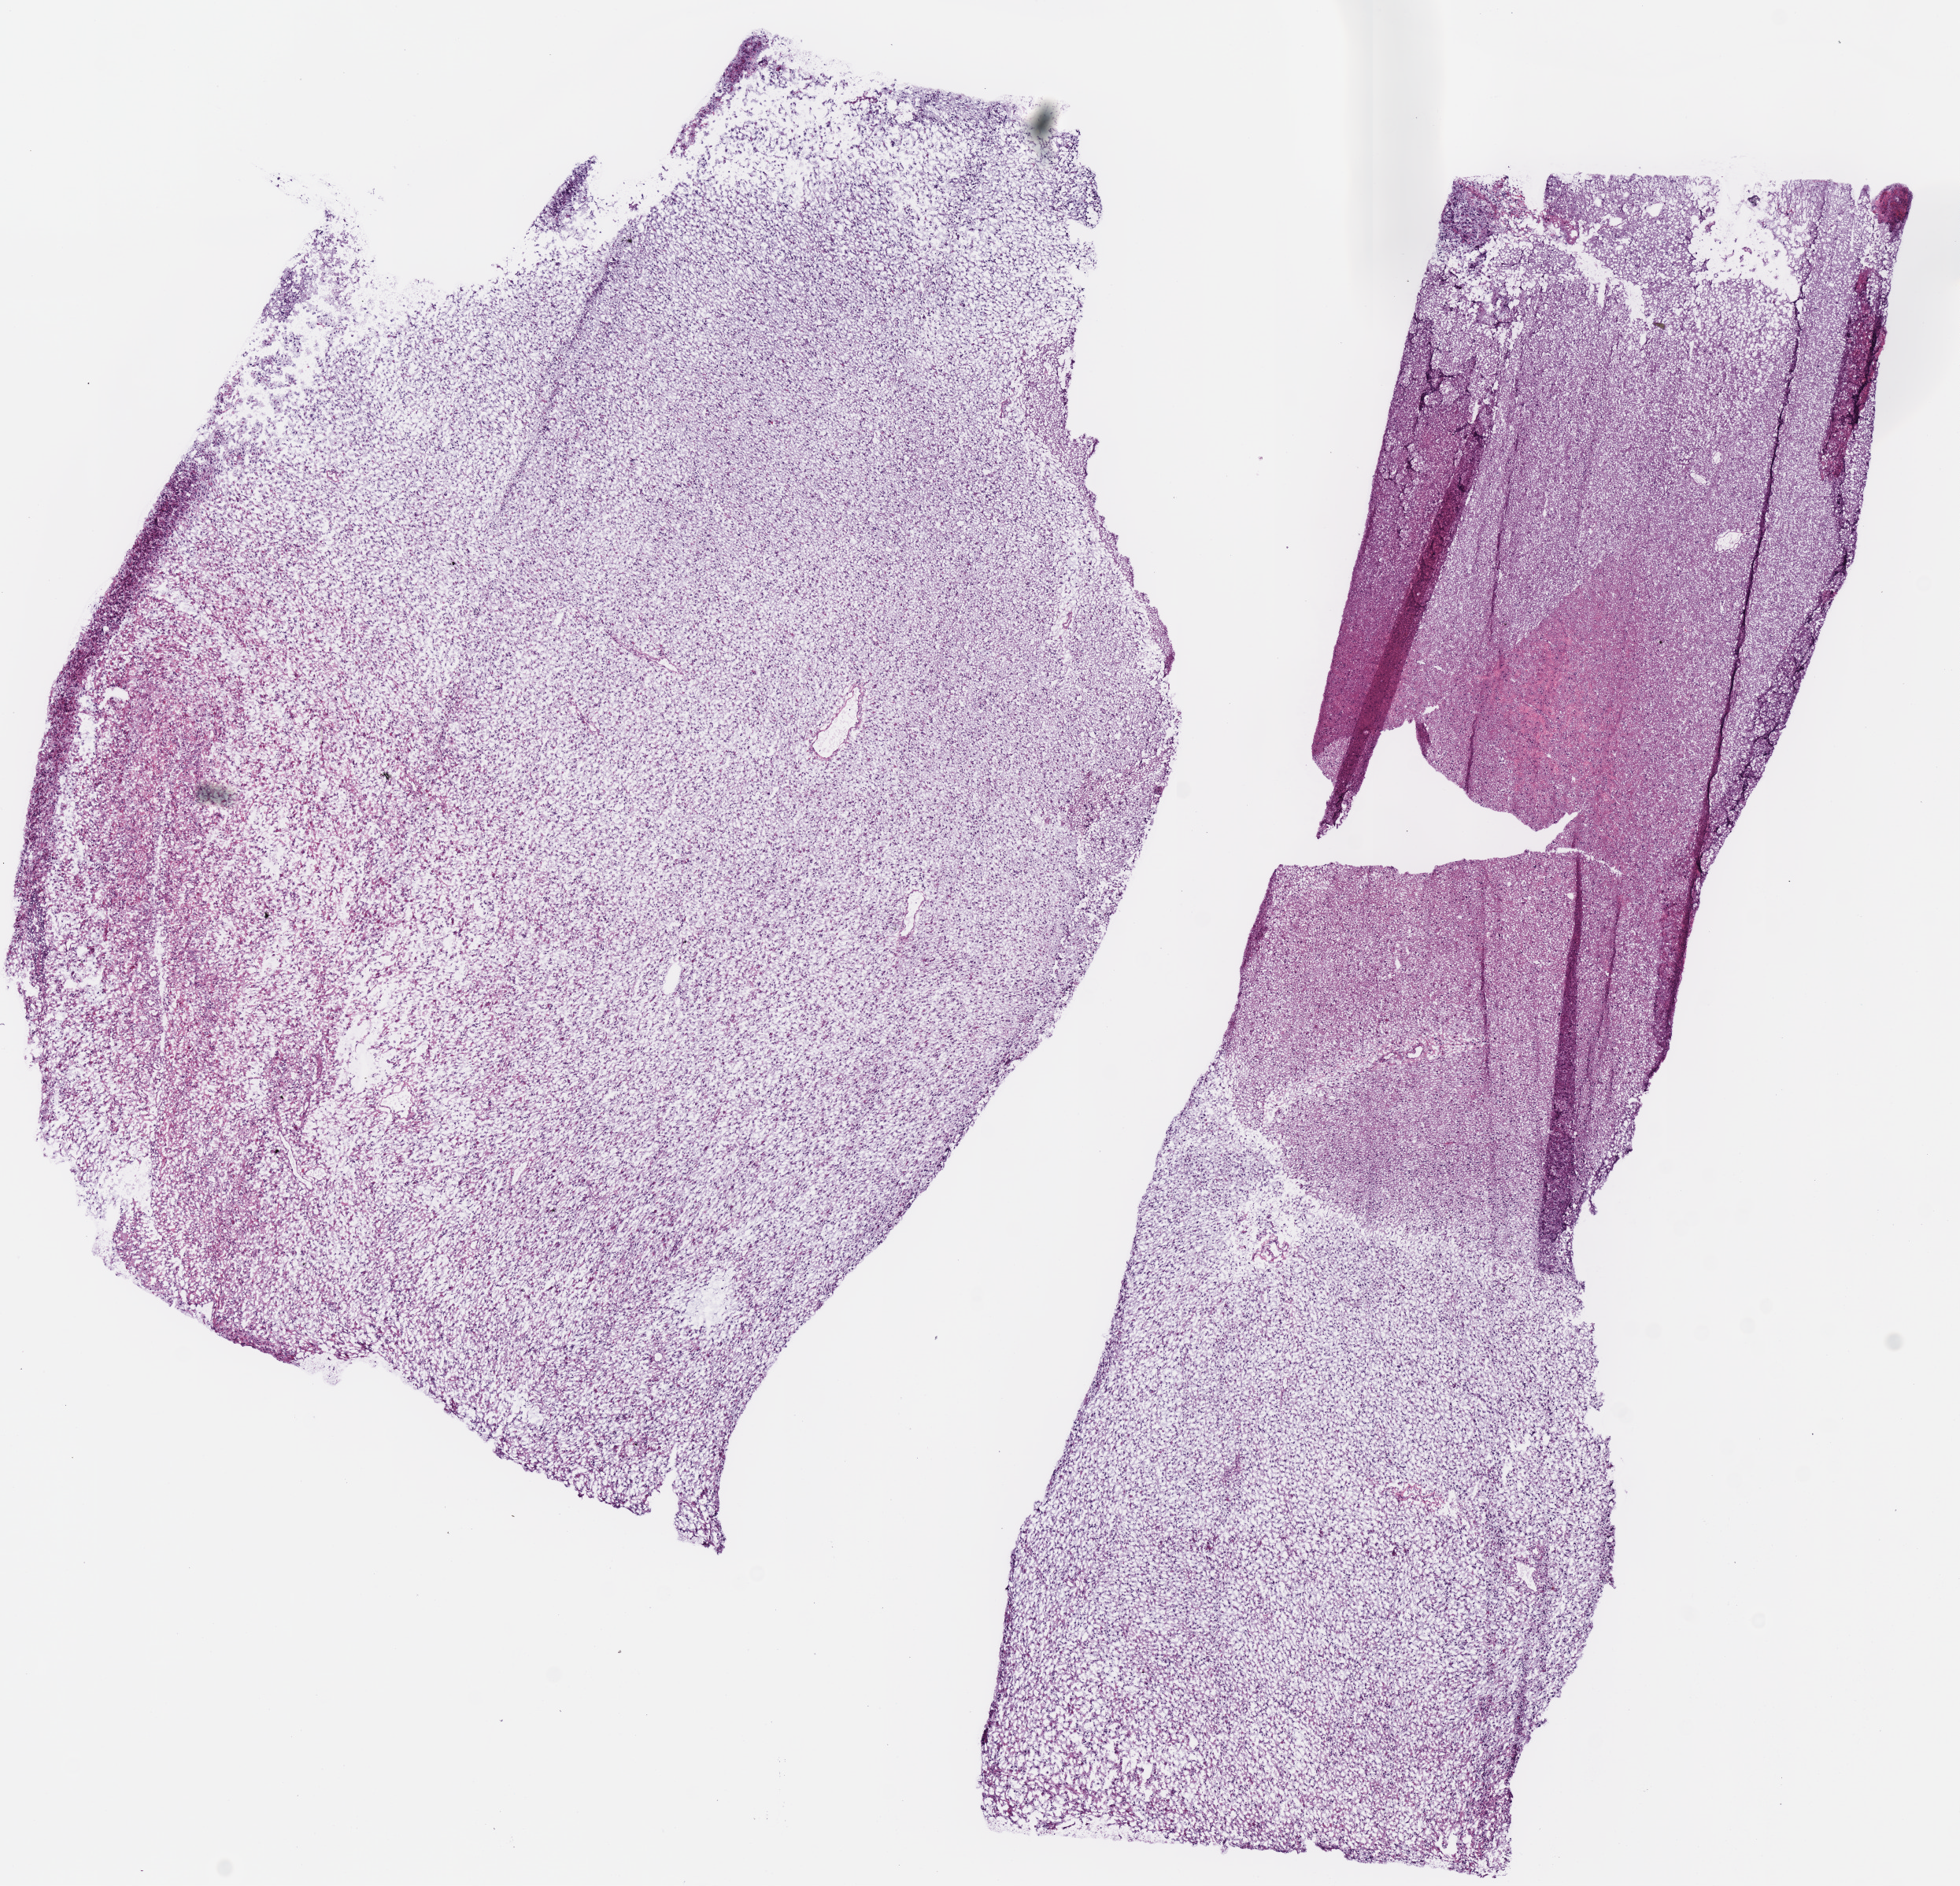
Digitized Hematoxylin and eosin (H&E) stained tissue section (whole slide) — a low-resolution overview of the entire scanned area, about 9.8 x 9.4 mm (slide scanned at 40x). Frozen section from the top of the tissue portion. Primary tumour sample from the brain. Male patient; age at initial diagnosis 29 years. Histologic grade: G3 (poorly differentiated). Composition of this section per pathologist review: tumour cells 85%, tumour nuclei 75%, normal cells 15%, stromal cells 0%, necrosis 0%.
Diagnosis: Mixed glioma (cerebrum). Laterality: right.